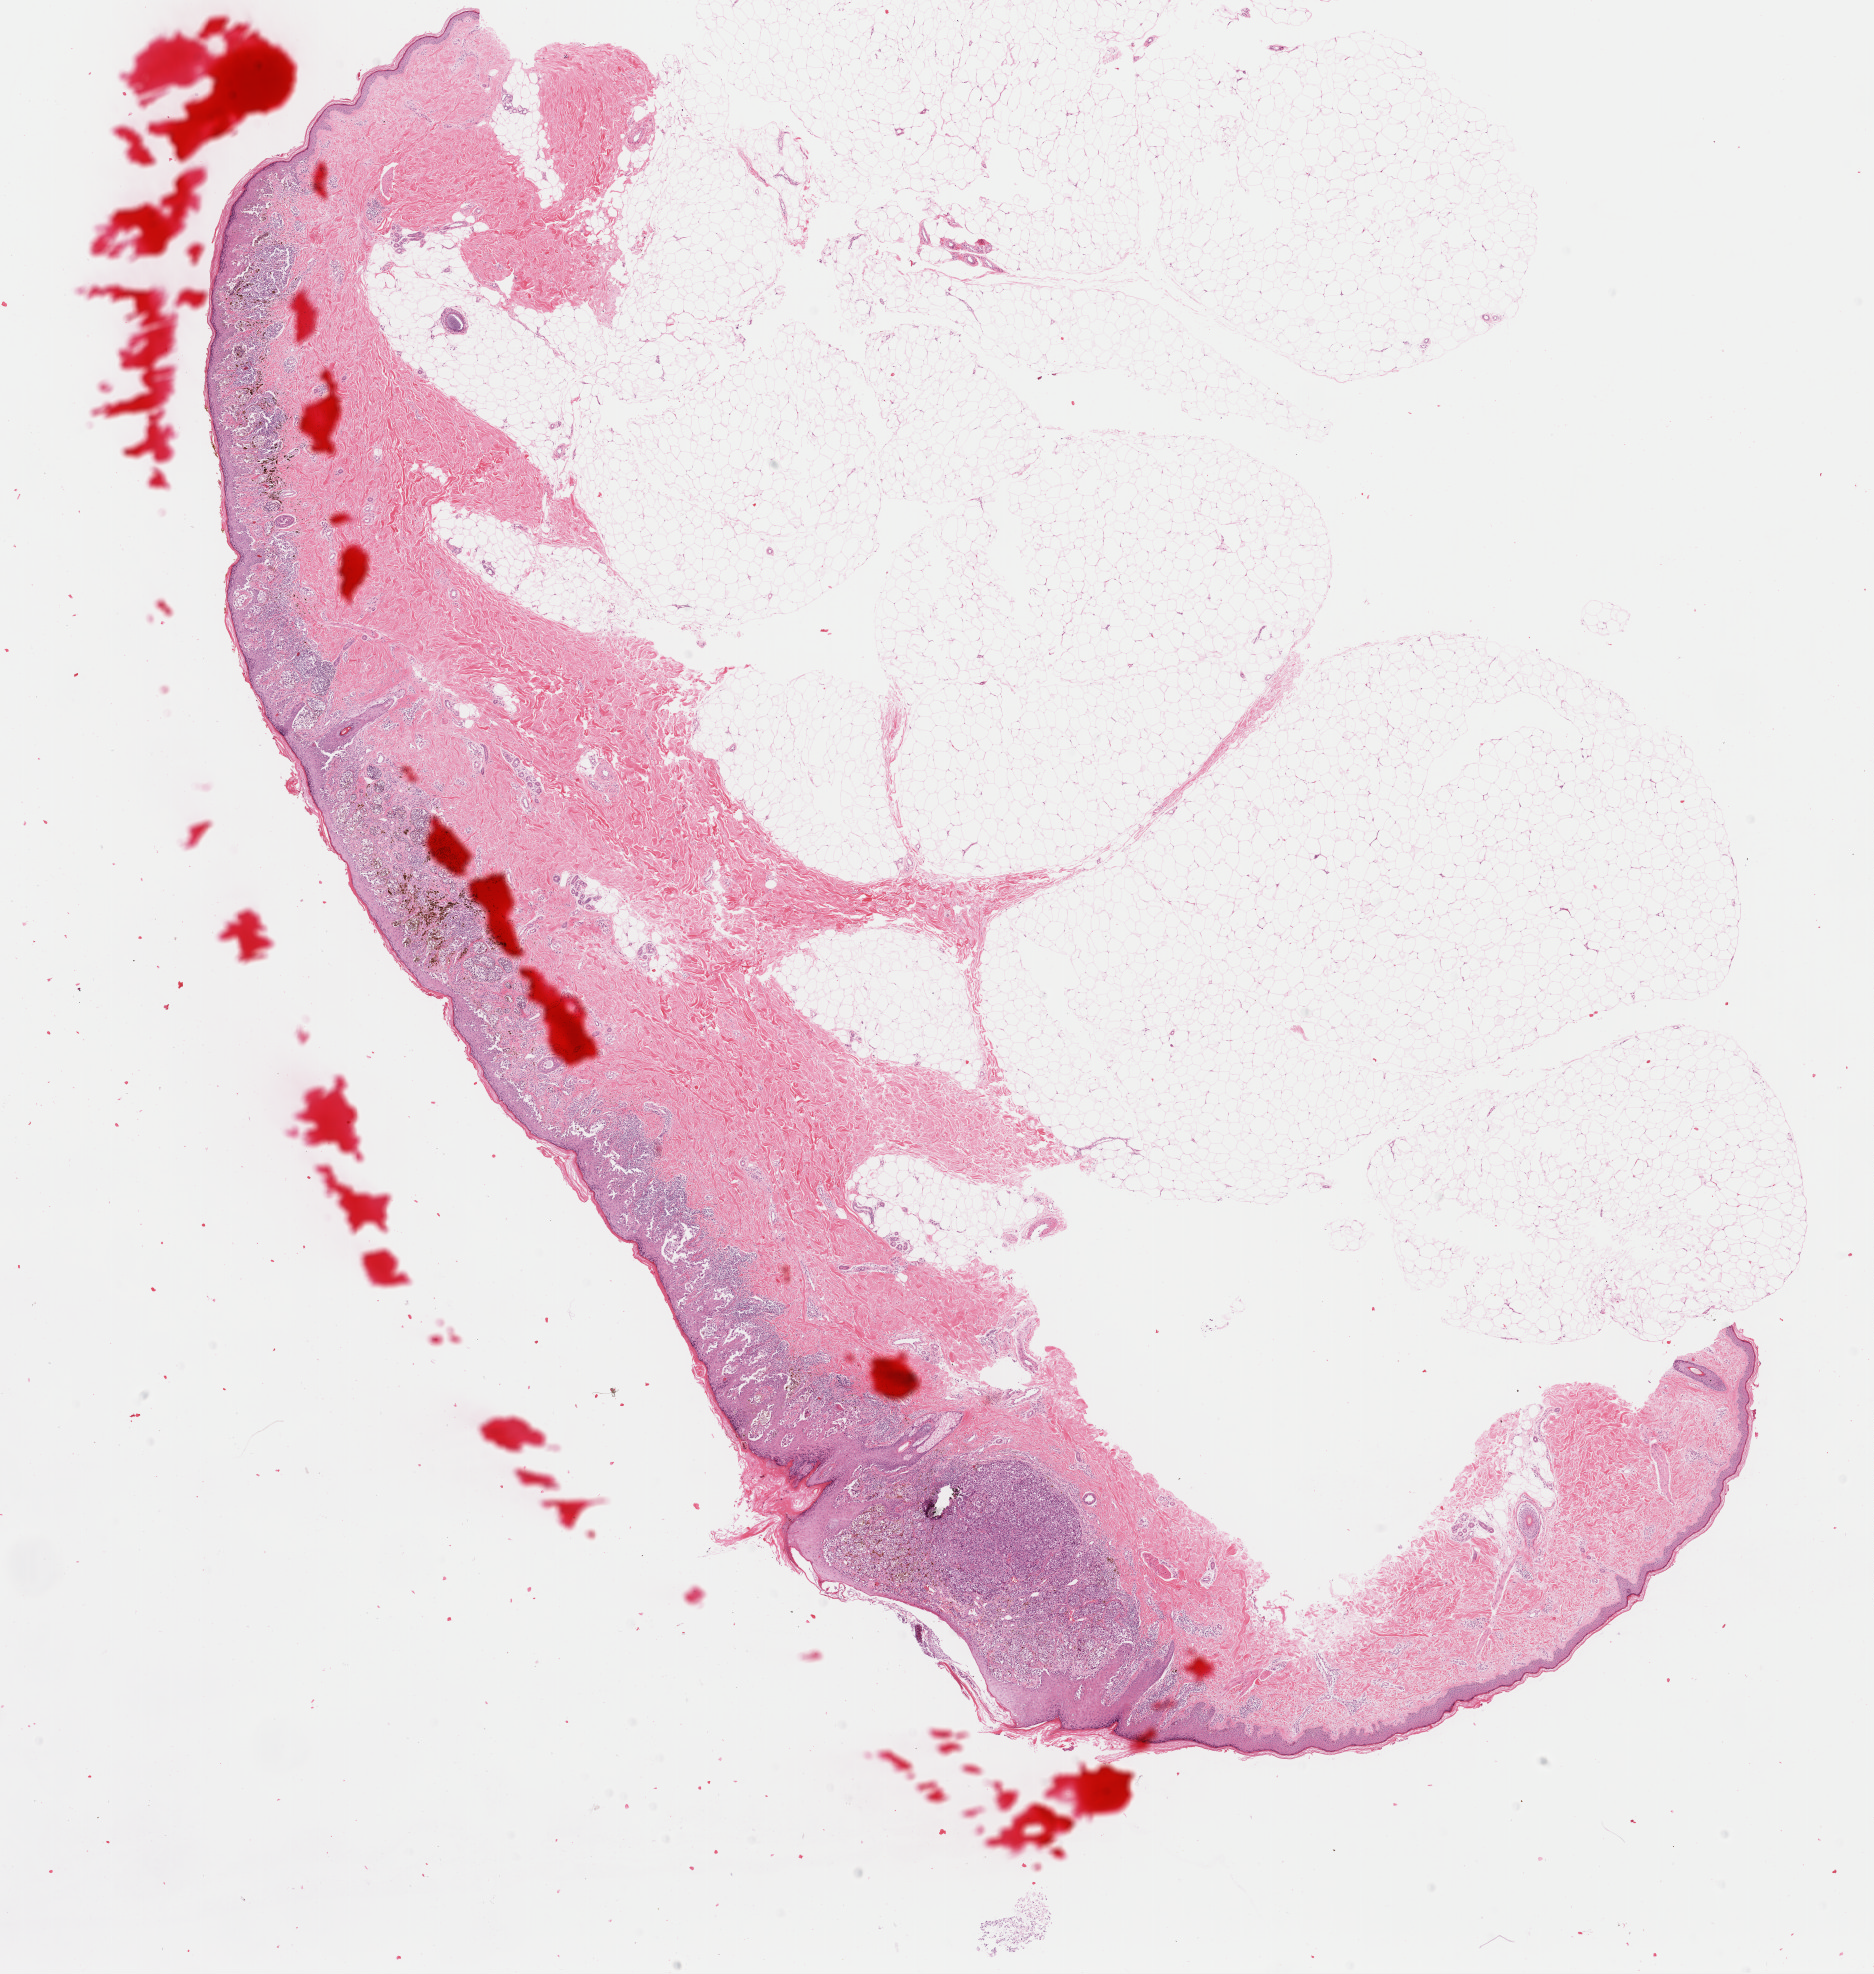
Digitized H&E tissue section (whole slide), low-resolution overview of the scanned area, about 14.8 x 15.6 mm; formalin-fixed paraffin-embedded (FFPE) diagnostic section; primary tumour sample from the skin. Patient: female, age at initial diagnosis 53 years.
Histologic diagnosis: Malignant melanoma, NOS.